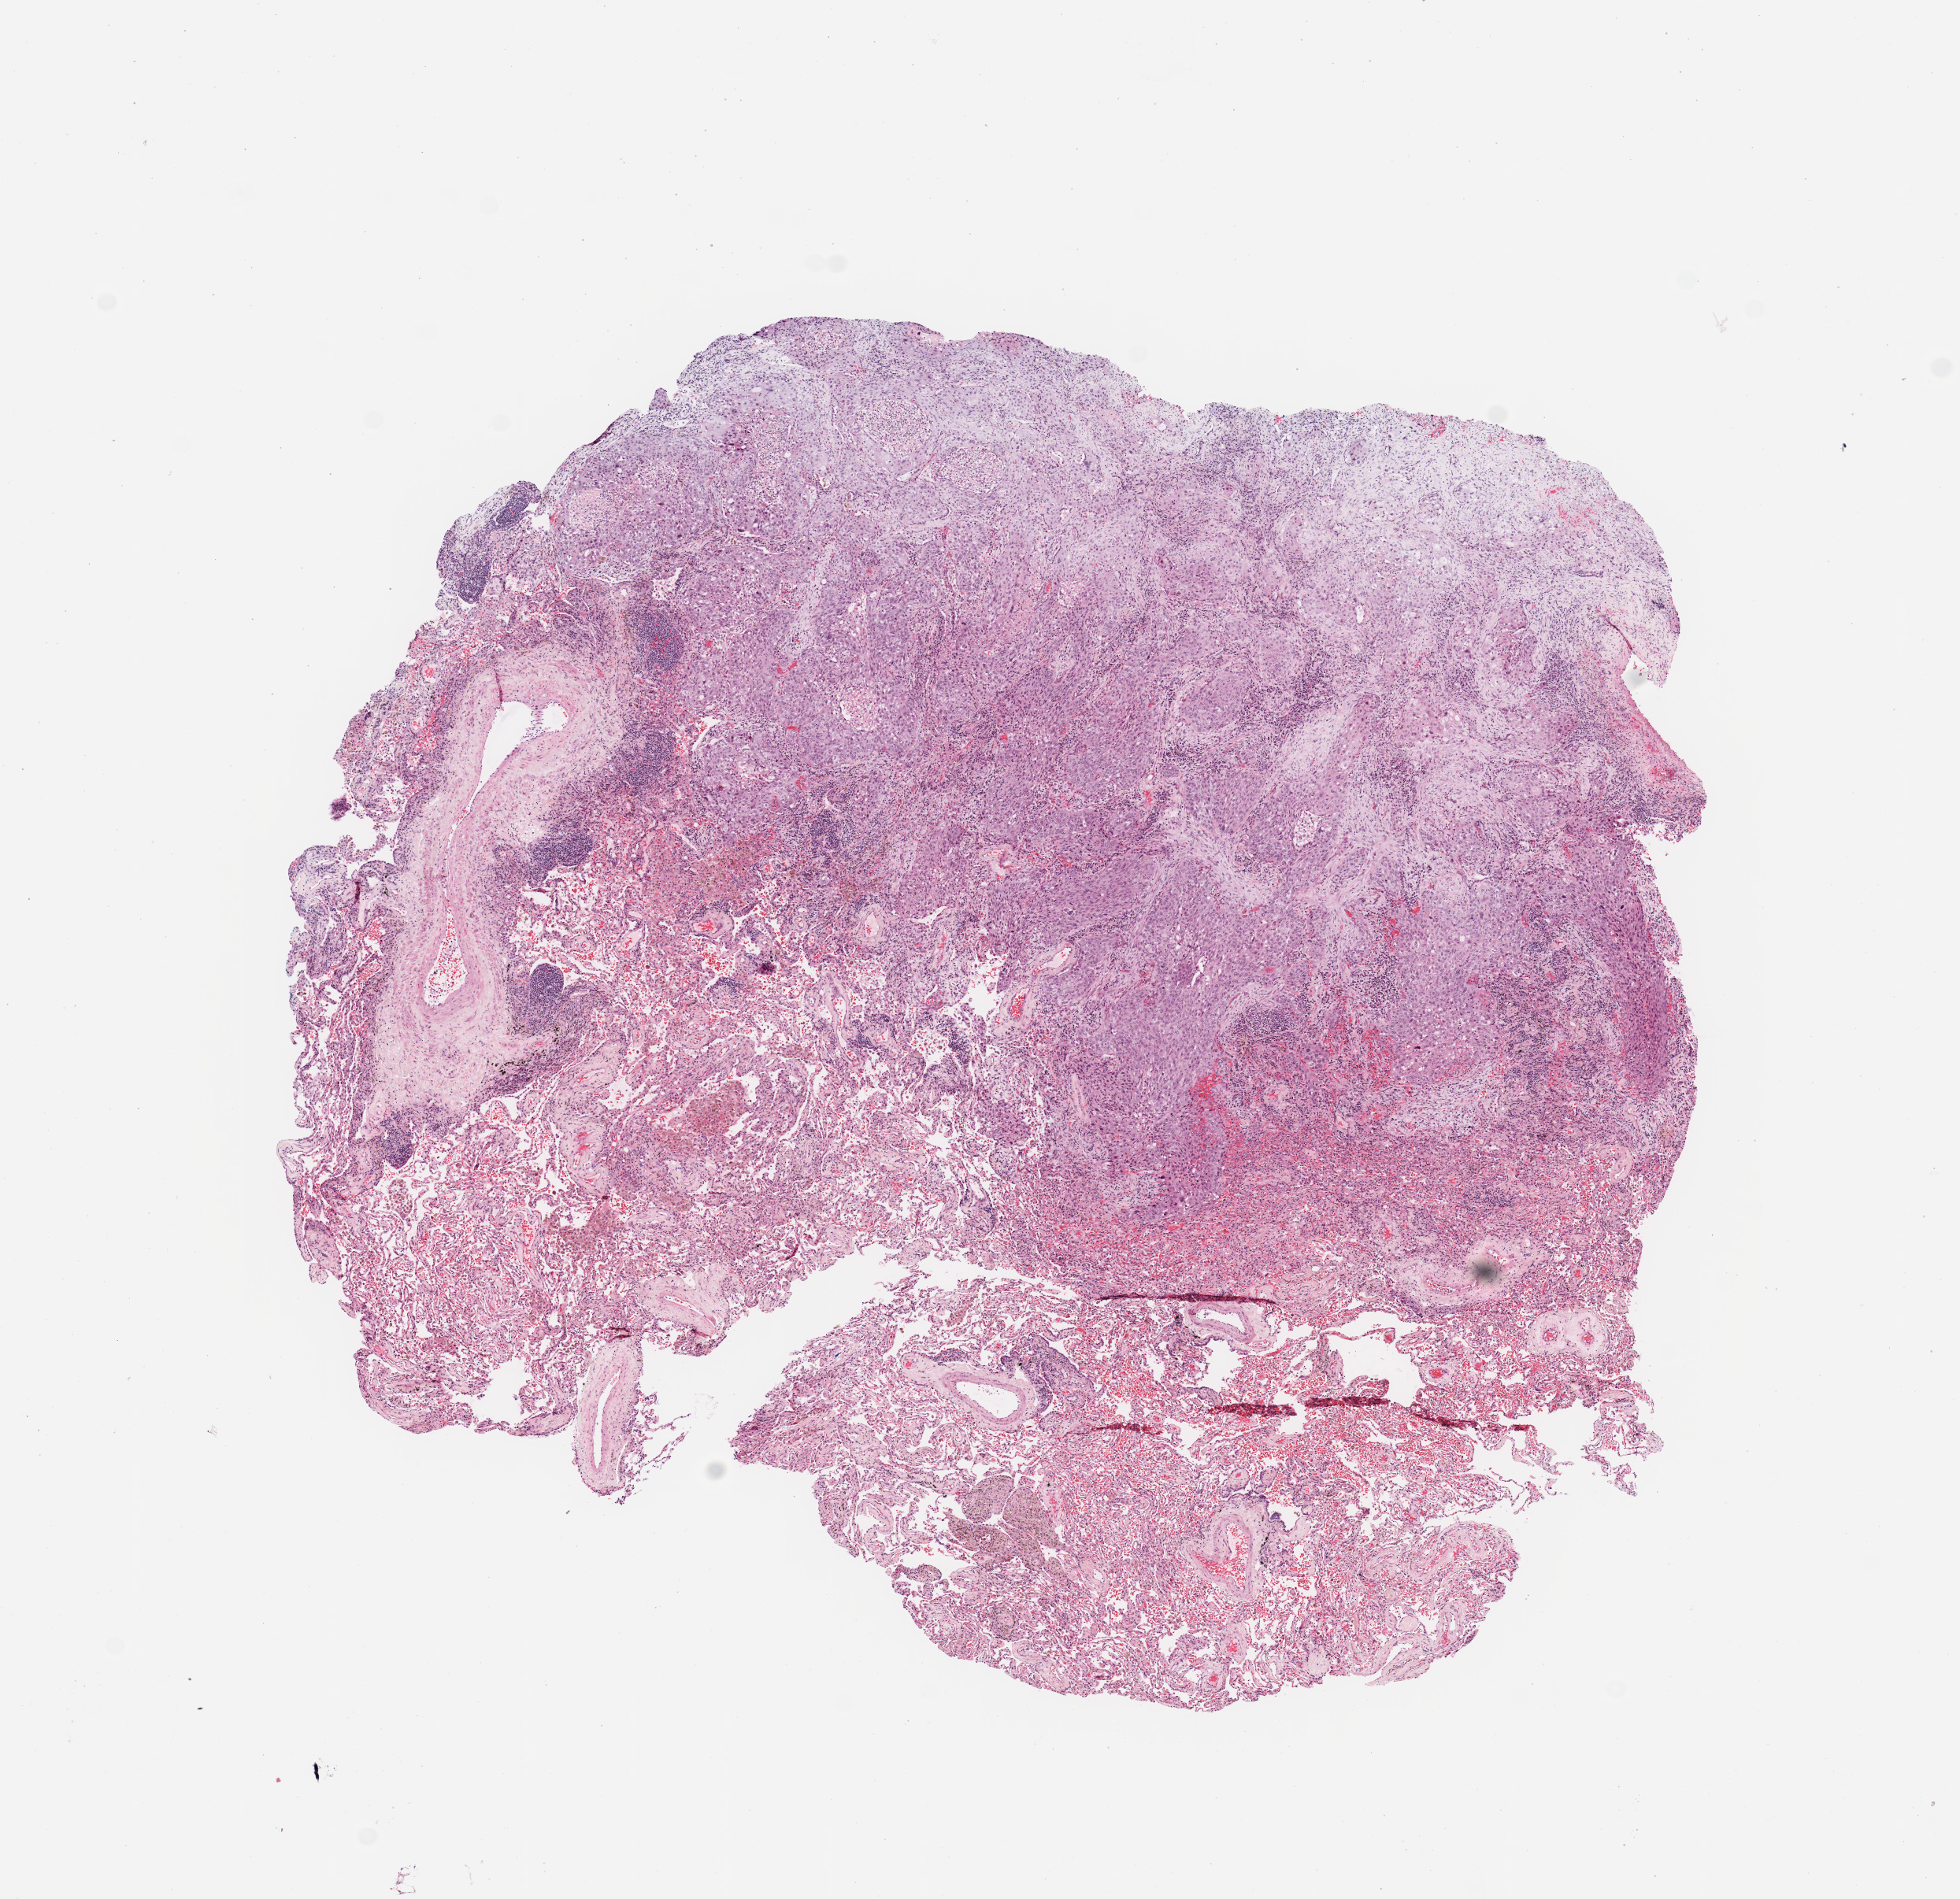
Whole-slide histology image, Hematoxylin and eosin (H&E) stained — low-resolution overview of the scanned area, about 9.8 x 9.5 mm; lung, tumour tissue. 71-year-old male patient. Histologic grade: G2 (moderately differentiated).
AJCC pathologic stage: I. Histologic diagnosis: Squamous cell carcinoma, NOS. Primary tumour site (as recorded): left lower lobe.